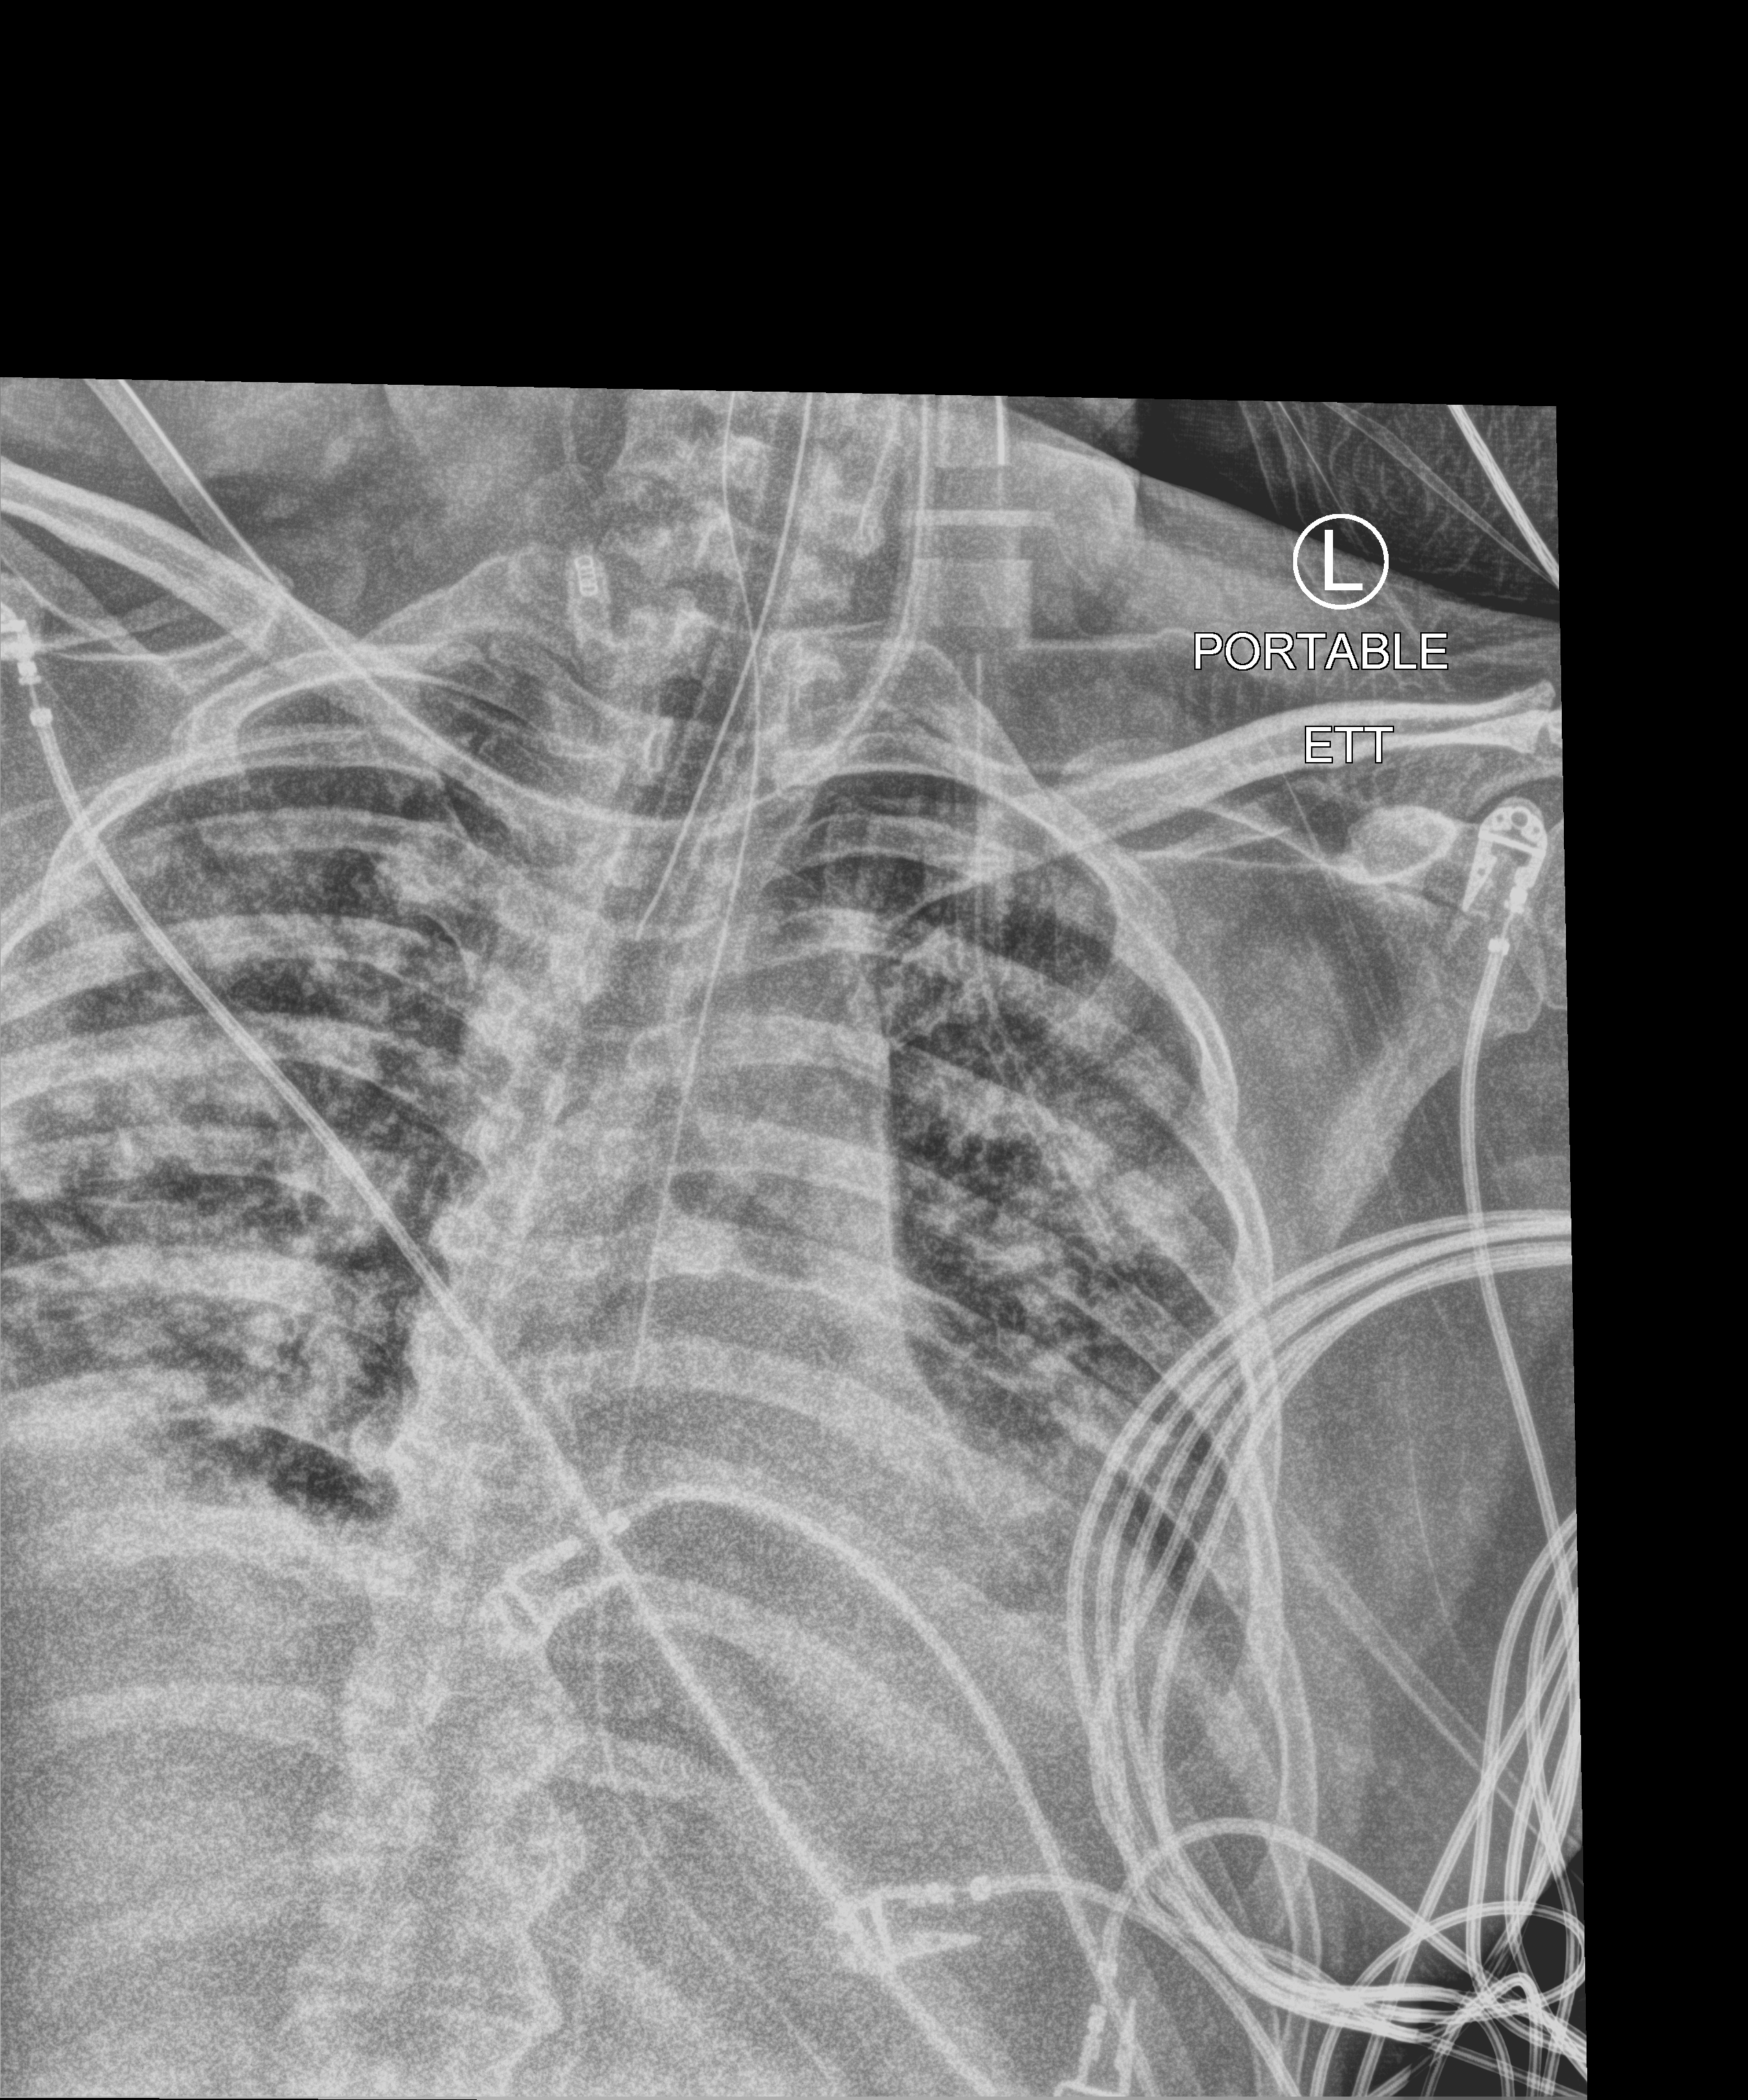
Bedside chest radiograph (computed radiography), anteroposterior (AP) projection. Patient hospitalised with COVID-19; male, aged 18–59 years.
Hospital-stay facts (about this admission, not read from this image; timing relative to this image not recorded):
- chronic kidney disease (admission record): no
- other chronic lung disease (admission record): no